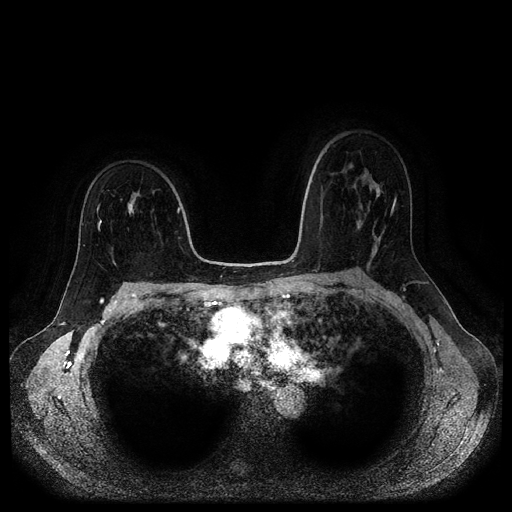
Breast MRI (dynamic contrast-enhanced, multi-phase), one axial slice. Slice 66 of 116 in the series (ordered by position). Dynamic contrast-enhanced series, time point 2 of 5 at this slice position (early post-contrast). 1.5 T. TE 2.6 ms, TR 5.3 ms. 2 mm slice thickness. 512 × 512 image matrix, field of view 360 × 360 mm. Patient: female, 50 years.
Structures marked on this image (semi-automatic segmentation, software-assisted and operator-edited):
- breast lesion (labelled benign in the annotation): bounding box <127,191,141,217> (left, top, right, bottom; pixels)